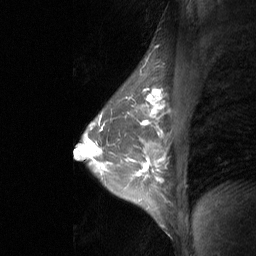
Breast MRI (dynamic contrast-enhanced), one sagittal slice; slice 46 of 64 in the series (ordered by position); dynamic contrast-enhanced study with each time point stored as its own series, time point 2 of 3 at this slice position (early post-contrast, ordered by acquisition time); 1.5 T; TE 4.8 ms, TR 27 ms; 2 mm slice thickness; 256 × 256 image matrix. Female patient, age 47 years. From the clinical record (not read from this slice): setting: breast cancer imaged before/during neoadjuvant chemotherapy; receptor status: HR-positive, HER2-negative.
Outlined on this slice (semi-automatic segmentation, software-assisted and operator-edited):
- analysis volume of interest (the breast-tissue region the enhancement analysis was run in; not a lesion): bounding box (x1, y1, x2, y2) in pixels: (120, 142, 162, 203)
- tumour enhancement mask (voxels above the 90 % enhancement threshold inside the analysis volume of interest): (137, 165, 148, 176)